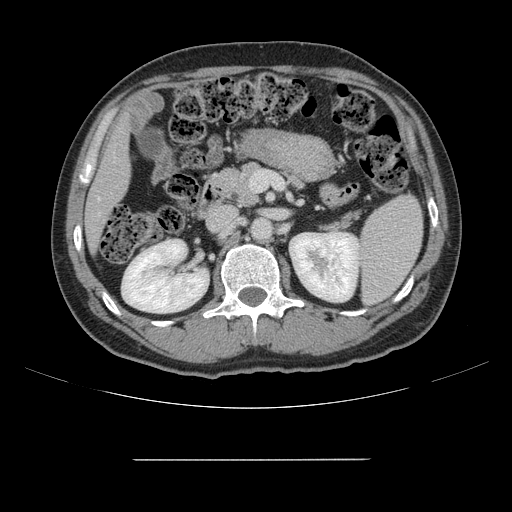
Contrast-enhanced abdominal CT, one axial slice; slice 67 of 164 in the series (ordered by position); 120 kVp; soft-tissue window (W 400 / L 40 HU); 512 × 512 image matrix, field of view 404 × 404 mm. Male patient, age 54 years. Case-level facts recorded for this patient, not image findings: diagnosis: colorectal cancer liver metastases, imaged before liver resection; multiple liver metastases: yes; largest metastasis: 1 cm.
Annotated regions visible in this slice (expert manual segmentation):
- hepatic veins: box from (x=98, y=198) to (x=101, y=201) px
- liver: (x=86, y=121)–(x=129, y=247)
- planned liver remnant (the part of the liver to remain after resection): (x=86, y=120)–(x=129, y=248)